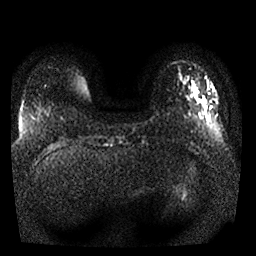
Breast MRI, one axial slice. Slice 3 of 25 in the series (ordered by position). Diffusion-weighted series; image 2 of 4 stored at this slice position (different b-values; order by instance number). 1.5 T. 4 mm slice thickness. 256 × 256 image matrix. Female patient.
Outlined on this slice (expert manual segmentation):
- tumour on diffusion-weighted imaging: bounding box <200,100,206,104> (left, top, right, bottom; pixels)